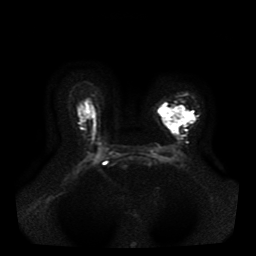
Breast MRI, one axial slice. Position 27 of 41 along the scan axis. Diffusion-weighted series; image 2 of 4 stored at this slice position (different b-values; order by instance number). 1.5 T. 5 mm slice thickness. 256 × 256 image matrix, field of view 330 × 330 mm. Female patient.
Outlined on this slice (outlined manually by an expert reader):
- tumour on diffusion-weighted imaging: box from (x=159, y=107) to (x=190, y=134) px